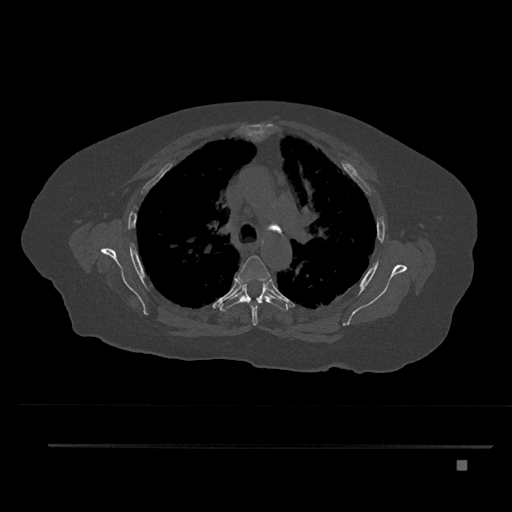
CT including the spine, one axial slice; slice 583 of 797 in the series (ordered by position); bone window (W 1800 / L 400 HU); 0.5 mm slice thickness; 512 × 512 image matrix. Female patient, age 76 years. From the clinical record (not read from this slice): primary cancer: lung; vertebrae with lytic lesions (as recorded): T11, L3.
Structures marked on this image (semi-automatically segmented with operator editing):
- T4 vertebra: bounding box [x1, y1, x2, y2] px = [236, 255, 270, 326]
- T5 vertebra: [220, 280, 288, 311]